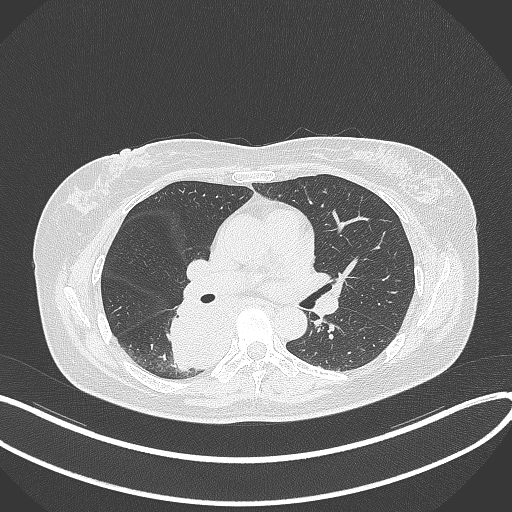
Chest CT, one axial slice. Slice 201 of 331 in the series (ordered by position). Reconstruction kernel B70f. 120 kVp. Lung window (W 1500 / L -600 HU). 512 × 512 image matrix. Patient: female, 54 years. From the clinical record (not read from this slice): clinical TNM (as recorded): T4 N0 M0.
Outlined on this slice (rectangle marked by the reading radiologist):
- lung tumour (recorded histology: adenocarcinoma): bounding box [x1, y1, x2, y2] px = [167, 298, 243, 371]